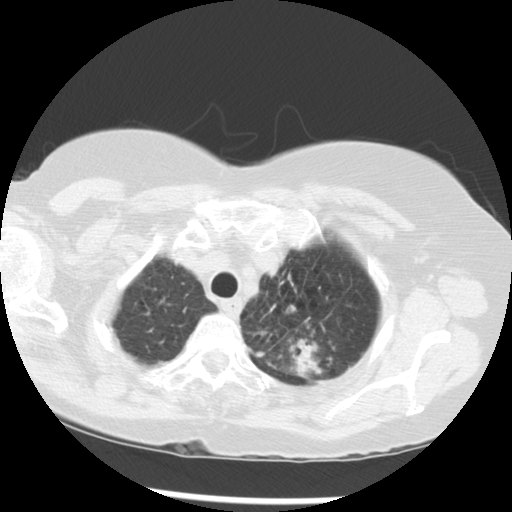
Low-dose screening chest CT, one axial slice. Position 243 of 283 along the scan axis. Reconstruction kernel STANDARD. Lung window (W 1500 / L -600 HU). 2.5 mm slice thickness. 512 × 512 image matrix.
Structures marked on this image (expert manual segmentation):
- lesion 1 (tumor, upper lobe of left lung): bounding box [x1, y1, x2, y2] px = [287, 339, 322, 377]